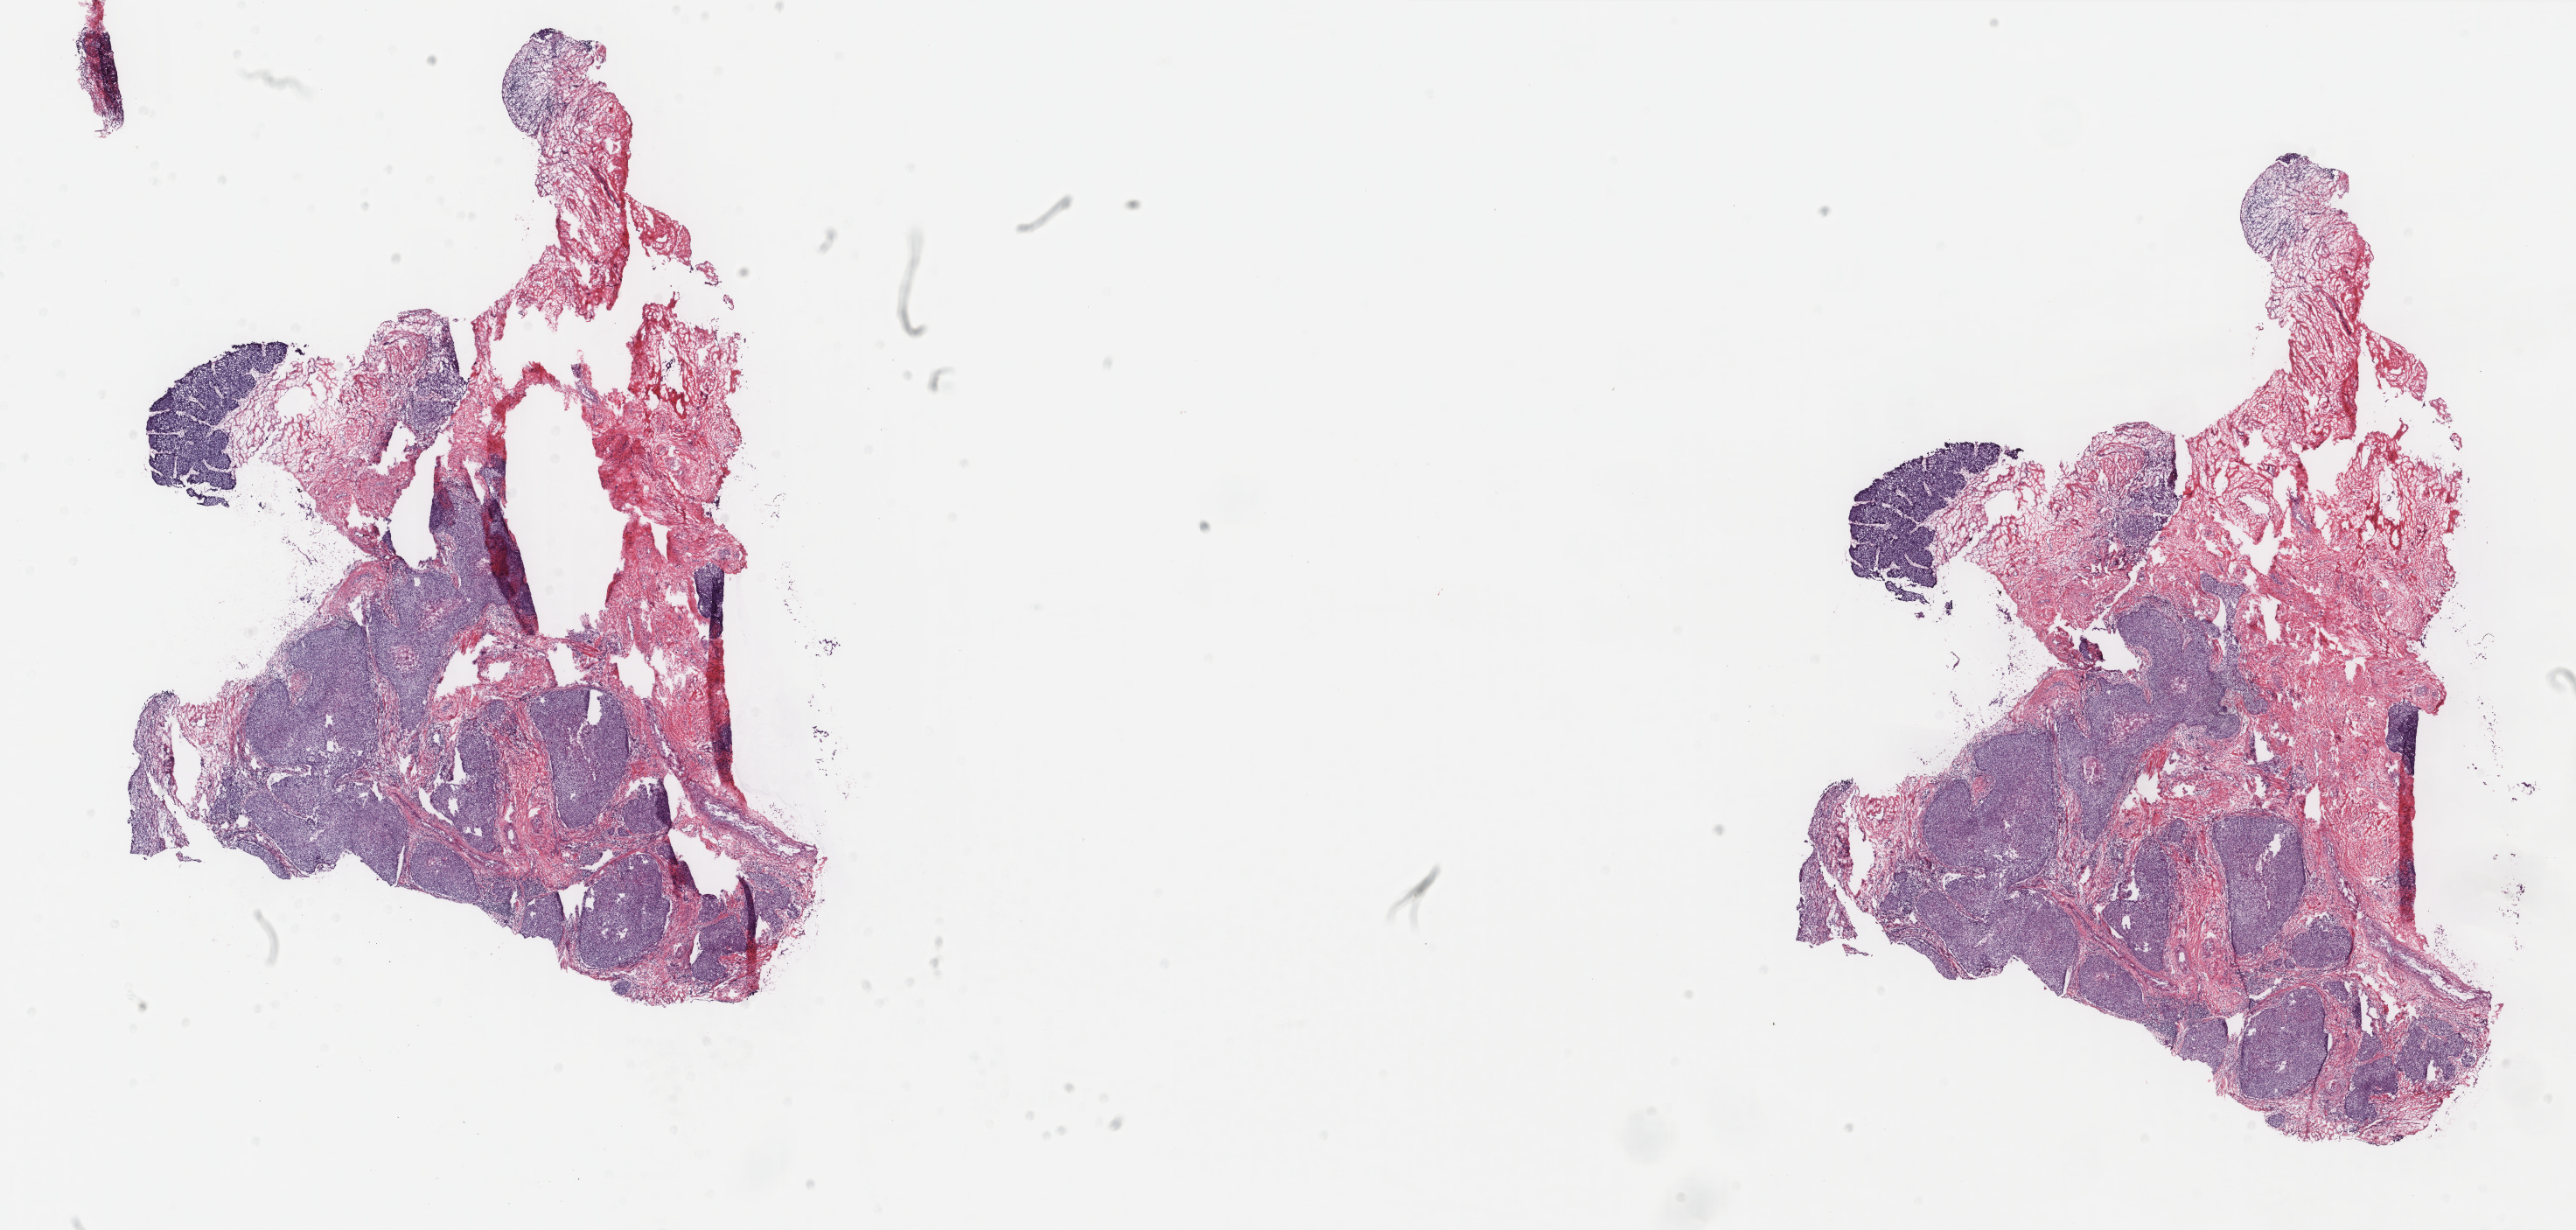
Whole-slide histology image, H&E-stained, shown as a low-resolution overview of the whole scanned area (about 23.4 x 11.2 mm). Frozen section from the top of the tissue portion. Sample: primary tumour, cervix. Patient: female, age at initial diagnosis 67 years. Histologic grade: G3 (poorly differentiated). Pathologist review of this section (percent, as recorded): tumour cells 50%, tumour nuclei 70%, normal cells 37%, stromal cells 10%, necrosis 3%. Infiltration values recorded for this section: lymphocyte infiltration 10%, monocyte infiltration 0%, neutrophil infiltration 0%.
Histologic diagnosis: Squamous cell carcinoma, large cell, nonkeratinizing, NOS. FIGO stage: IA2.